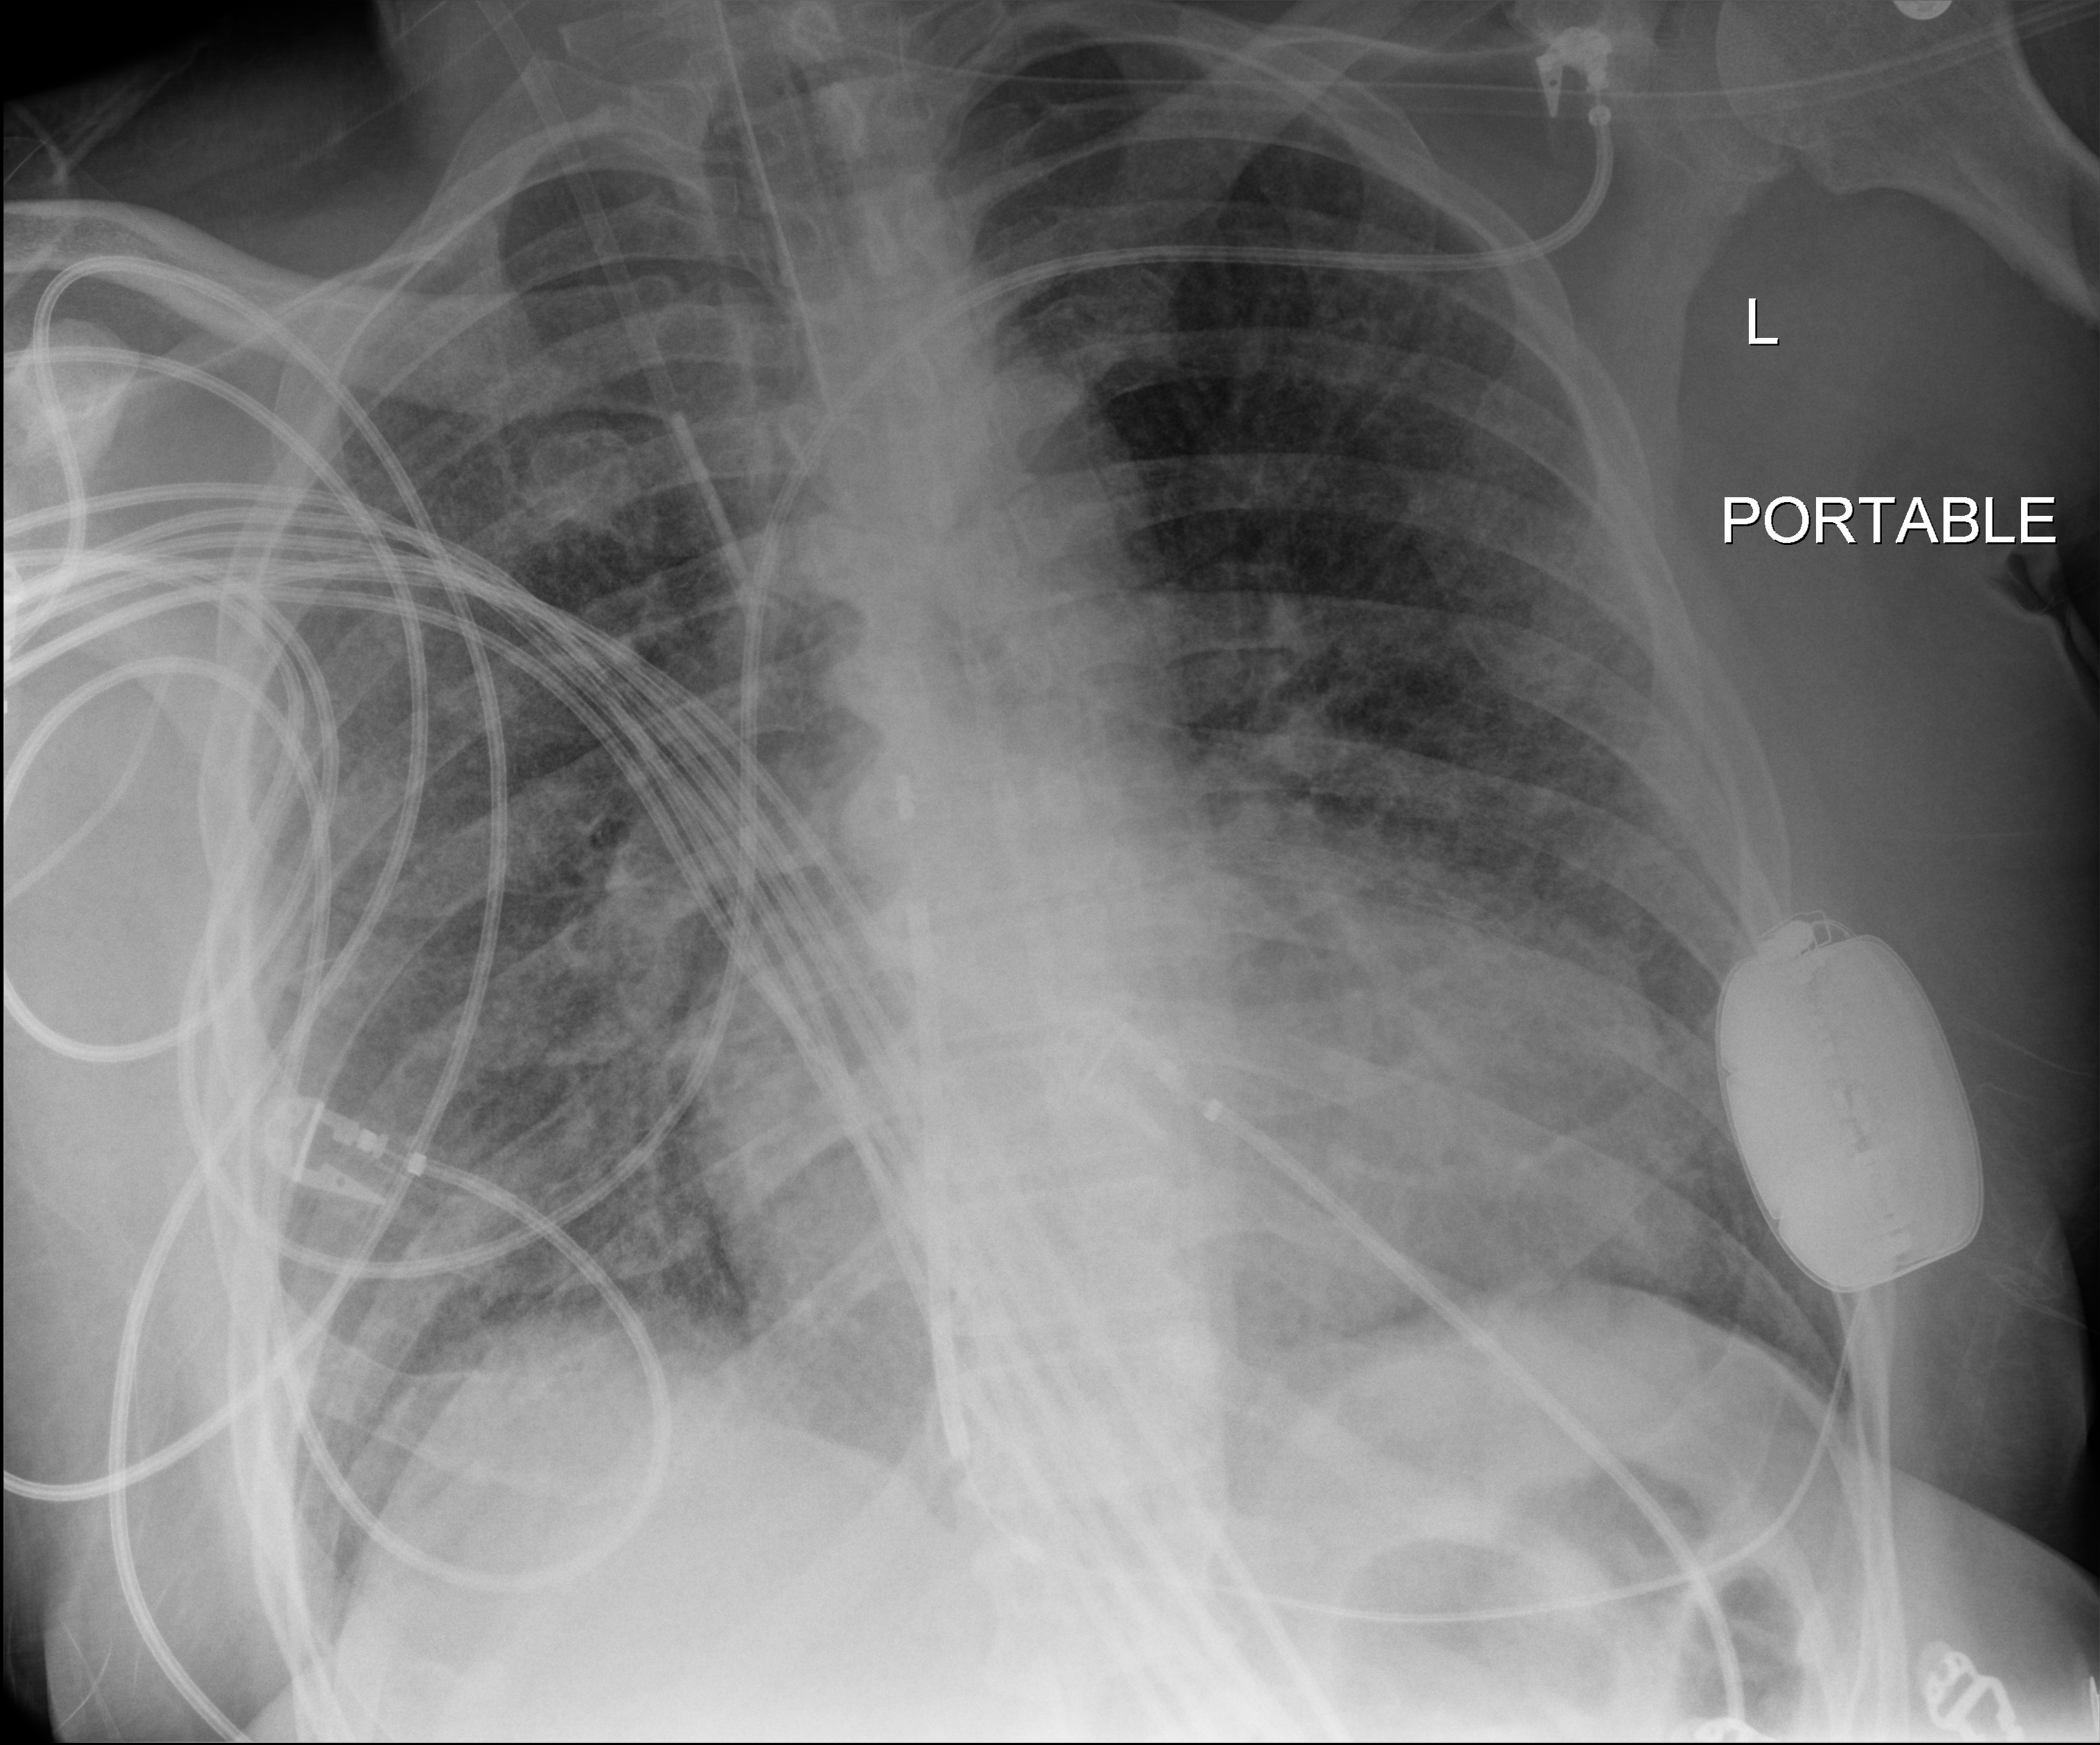
Portable chest radiograph, anteroposterior (AP) projection. Patient hospitalised with COVID-19; male, aged 60–74 years.
From the hospital-stay record, not from the radiograph (when in the stay this image was taken is not recorded): mechanically ventilated during this hospital stay: yes.